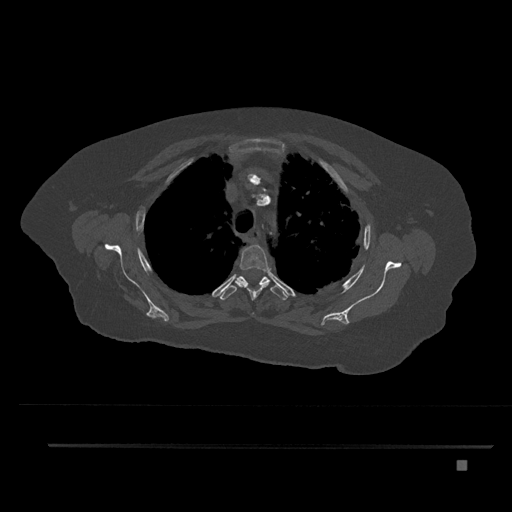
CT including the spine, one axial slice; slice 622 of 797 in the series (ordered by position); bone window (W 1800 / L 400 HU); 512 × 512 image matrix, field of view 437 × 437 mm. Female patient, age 76 years. From the clinical record (not read from this slice): primary cancer: lung; vertebrae with lytic lesions (as recorded): T11, L3.
Structures marked on this image (semi-automatic segmentation, software-assisted and operator-edited):
- T3 vertebra: bounding box <235,244,270,314> (left, top, right, bottom; pixels)
- T4 vertebra: <219,276,288,300>